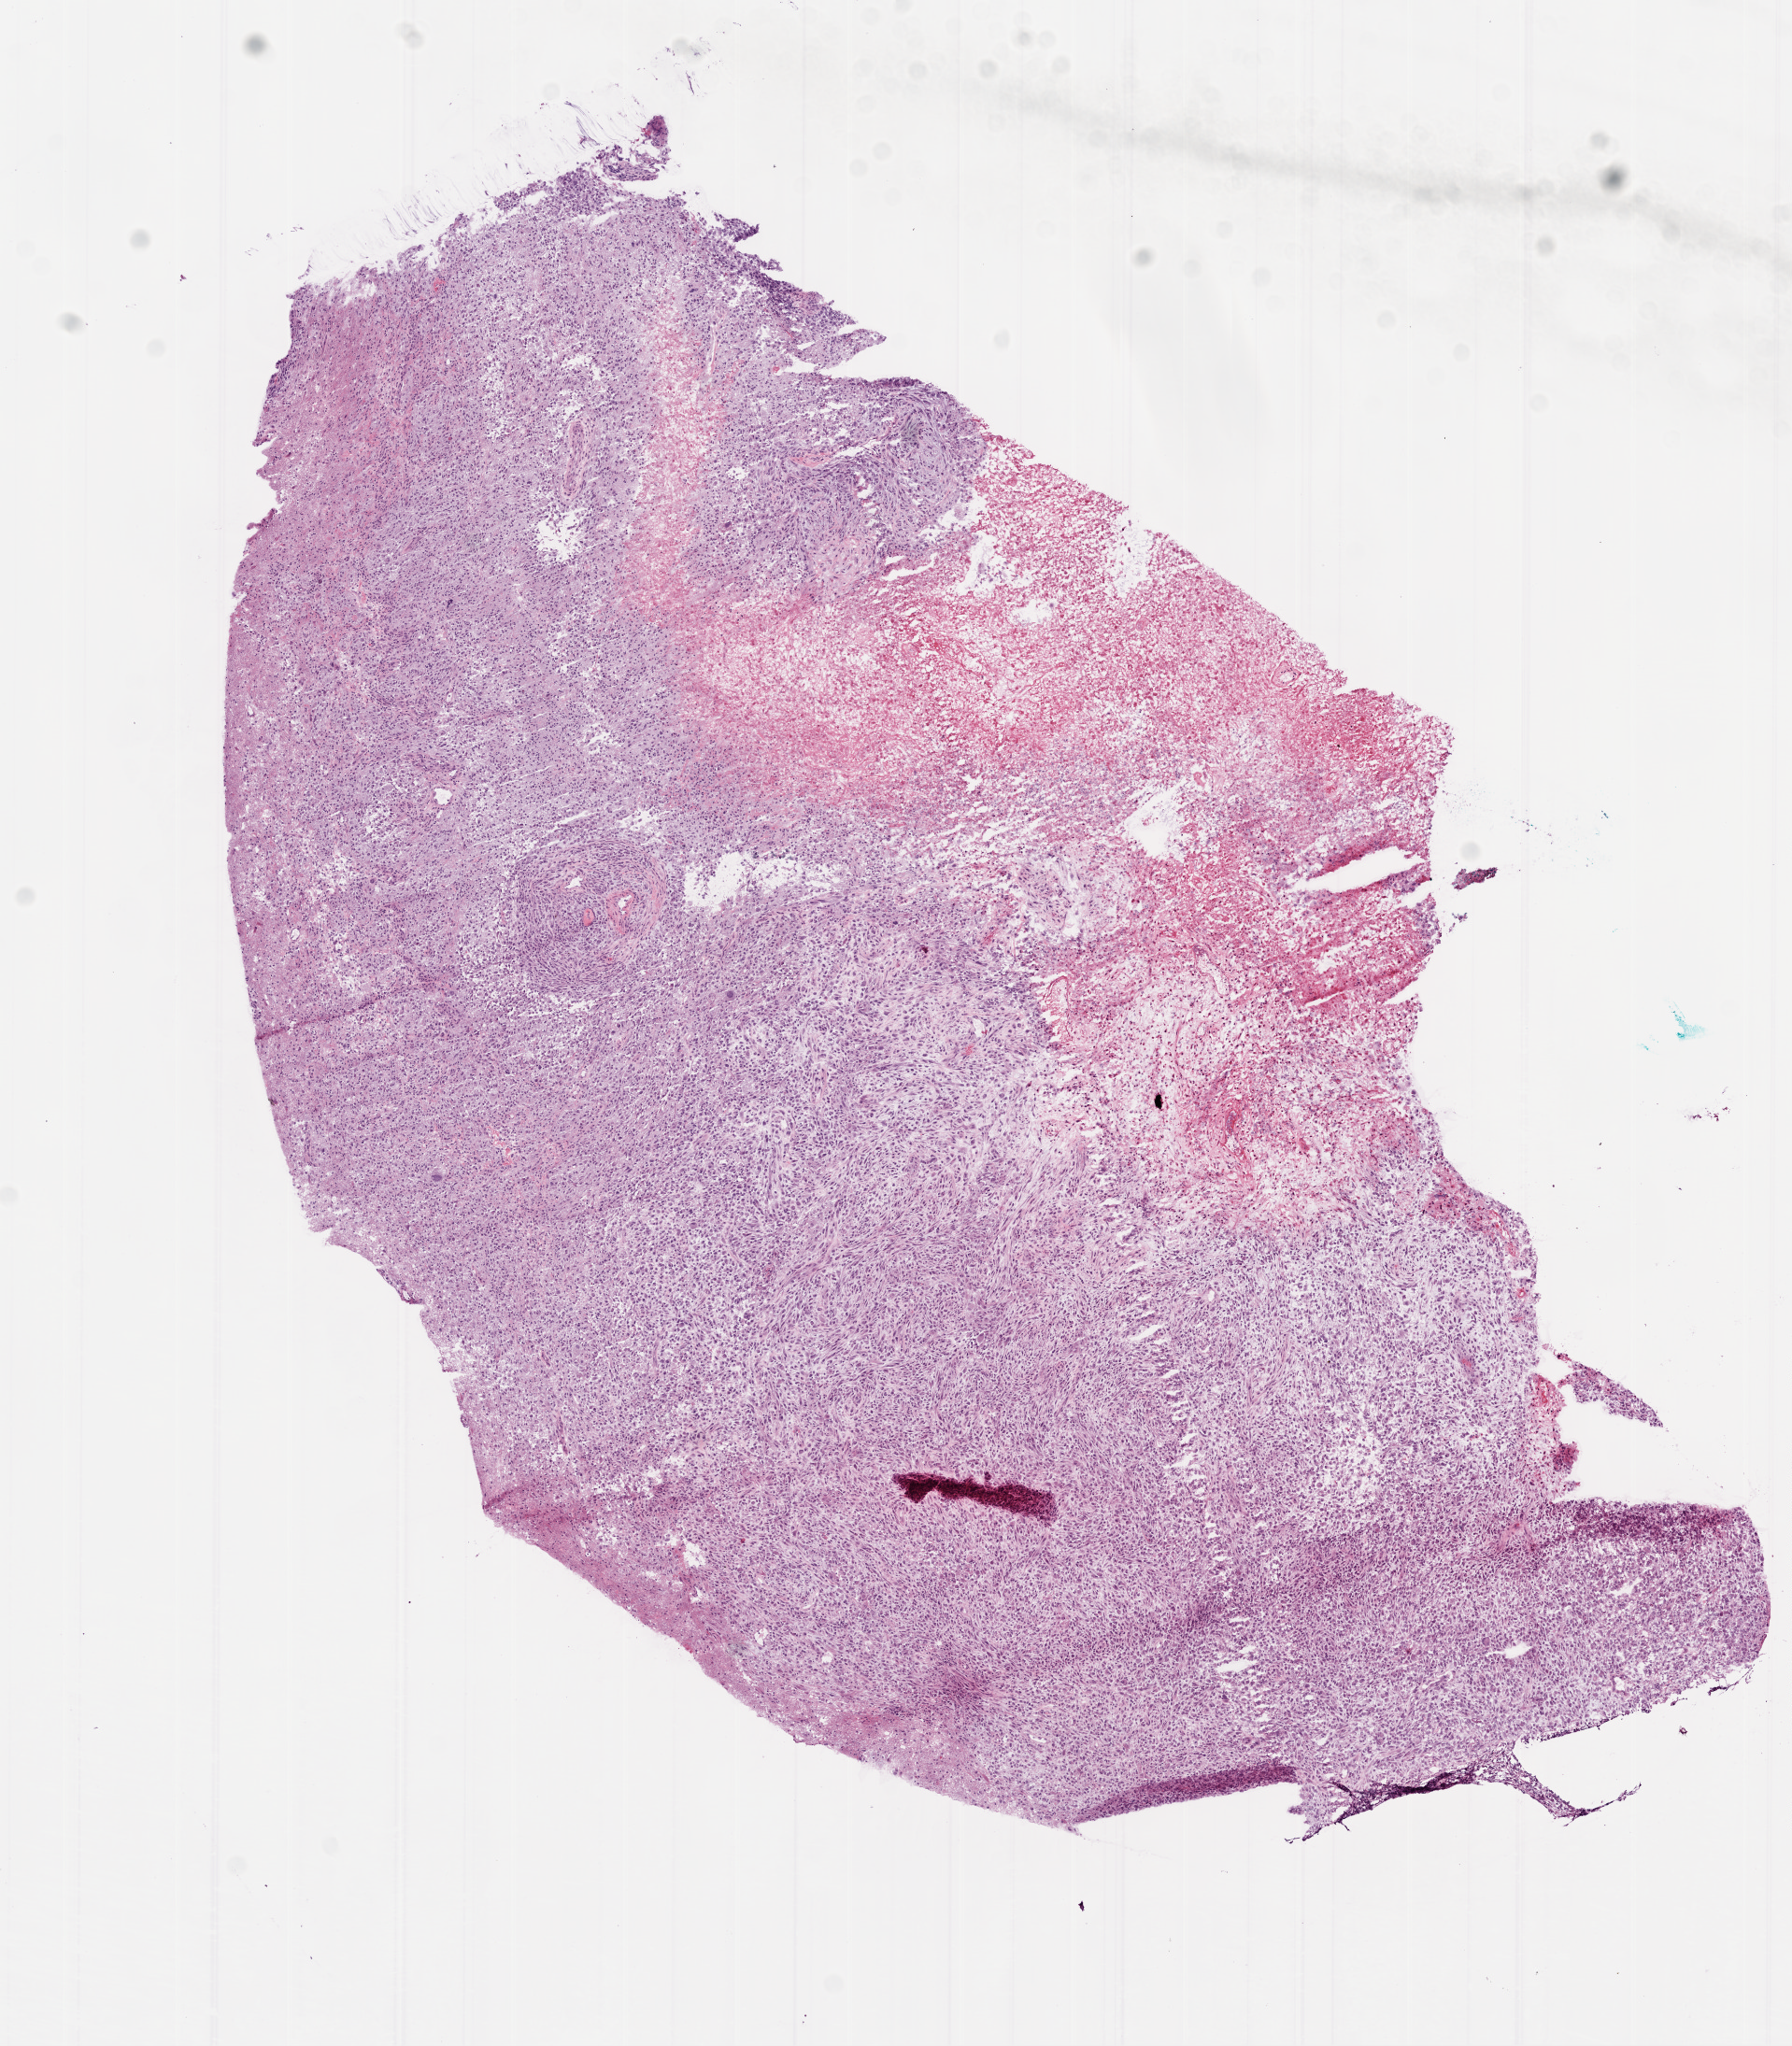
Hematoxylin and eosin (H&E) stained whole-slide image, whole scanned area (about 7.7 x 8.8 mm, from a 20x scan) shown as a low-resolution overview. Frozen section. Brain, primary tumour sample. Male, age 71 years at initial diagnosis. Slide review estimates, as recorded: tumour cells 70%, tumour nuclei 95%, normal cells 0%, stromal cells 10%, necrosis 20%.
Histologic diagnosis: Glioblastoma.